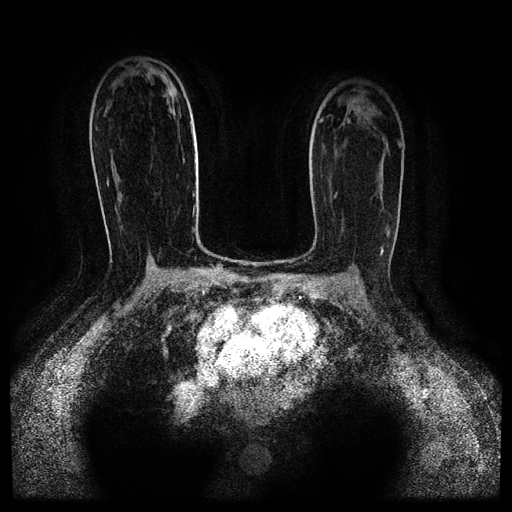
Breast MRI (dynamic contrast-enhanced, multi-phase), one axial slice. Position 62 of 116 along the scan axis. Dynamic contrast-enhanced series, time point 2 of 5 at this slice position (early post-contrast). 1.5 T. TE 2.6 ms, TR 5.3 ms. 2 mm slice thickness. 512 × 512 image matrix. Patient: female, 52 years.
Structures marked on this image (semi-automatic segmentation, software-assisted and operator-edited):
- breast lesion (labelled benign in the annotation): bounding box <171,88,174,93> (left, top, right, bottom; pixels)